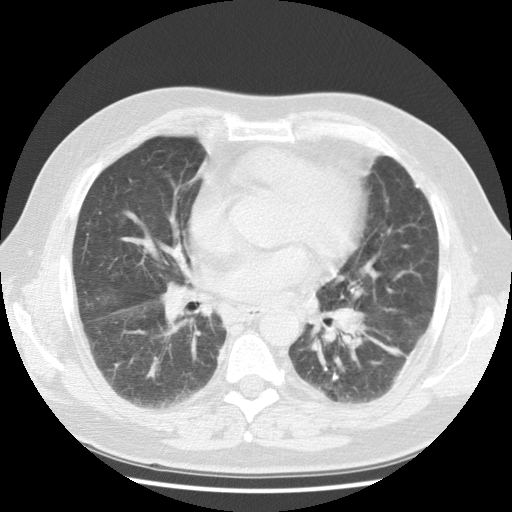
Low-dose screening chest CT, one axial slice; position 57 of 108 along the scan axis; reconstruction kernel STANDARD; lung window (W 1500 / L -600 HU); 2.5 mm slice thickness; 512 × 512 image matrix, field of view 350 × 350 mm.
Annotated regions visible in this slice (manually delineated by an expert):
- lesion 1 (tumor, hilum of left lung): bounding box [x1, y1, x2, y2] px = [334, 305, 365, 337]